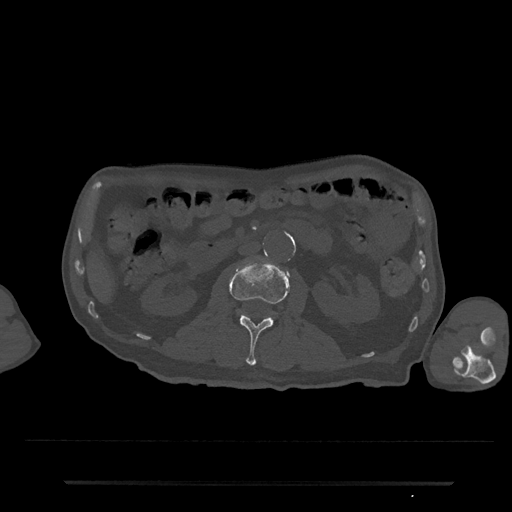
CT including the spine, one axial slice; position 43 of 797 along the scan axis; reconstruction kernel Br40s/3; 120 kVp; bone window (W 1800 / L 400 HU); 0.5 mm slice thickness; 512 × 512 image matrix, field of view 427 × 427 mm. Patient: male, 74 years. Case-level facts recorded for this patient, not image findings: primary cancer: prostate.
Annotated regions visible in this slice (semi-automatically segmented with operator editing):
- L2 vertebra: bounding box <228,258,290,366> (left, top, right, bottom; pixels)